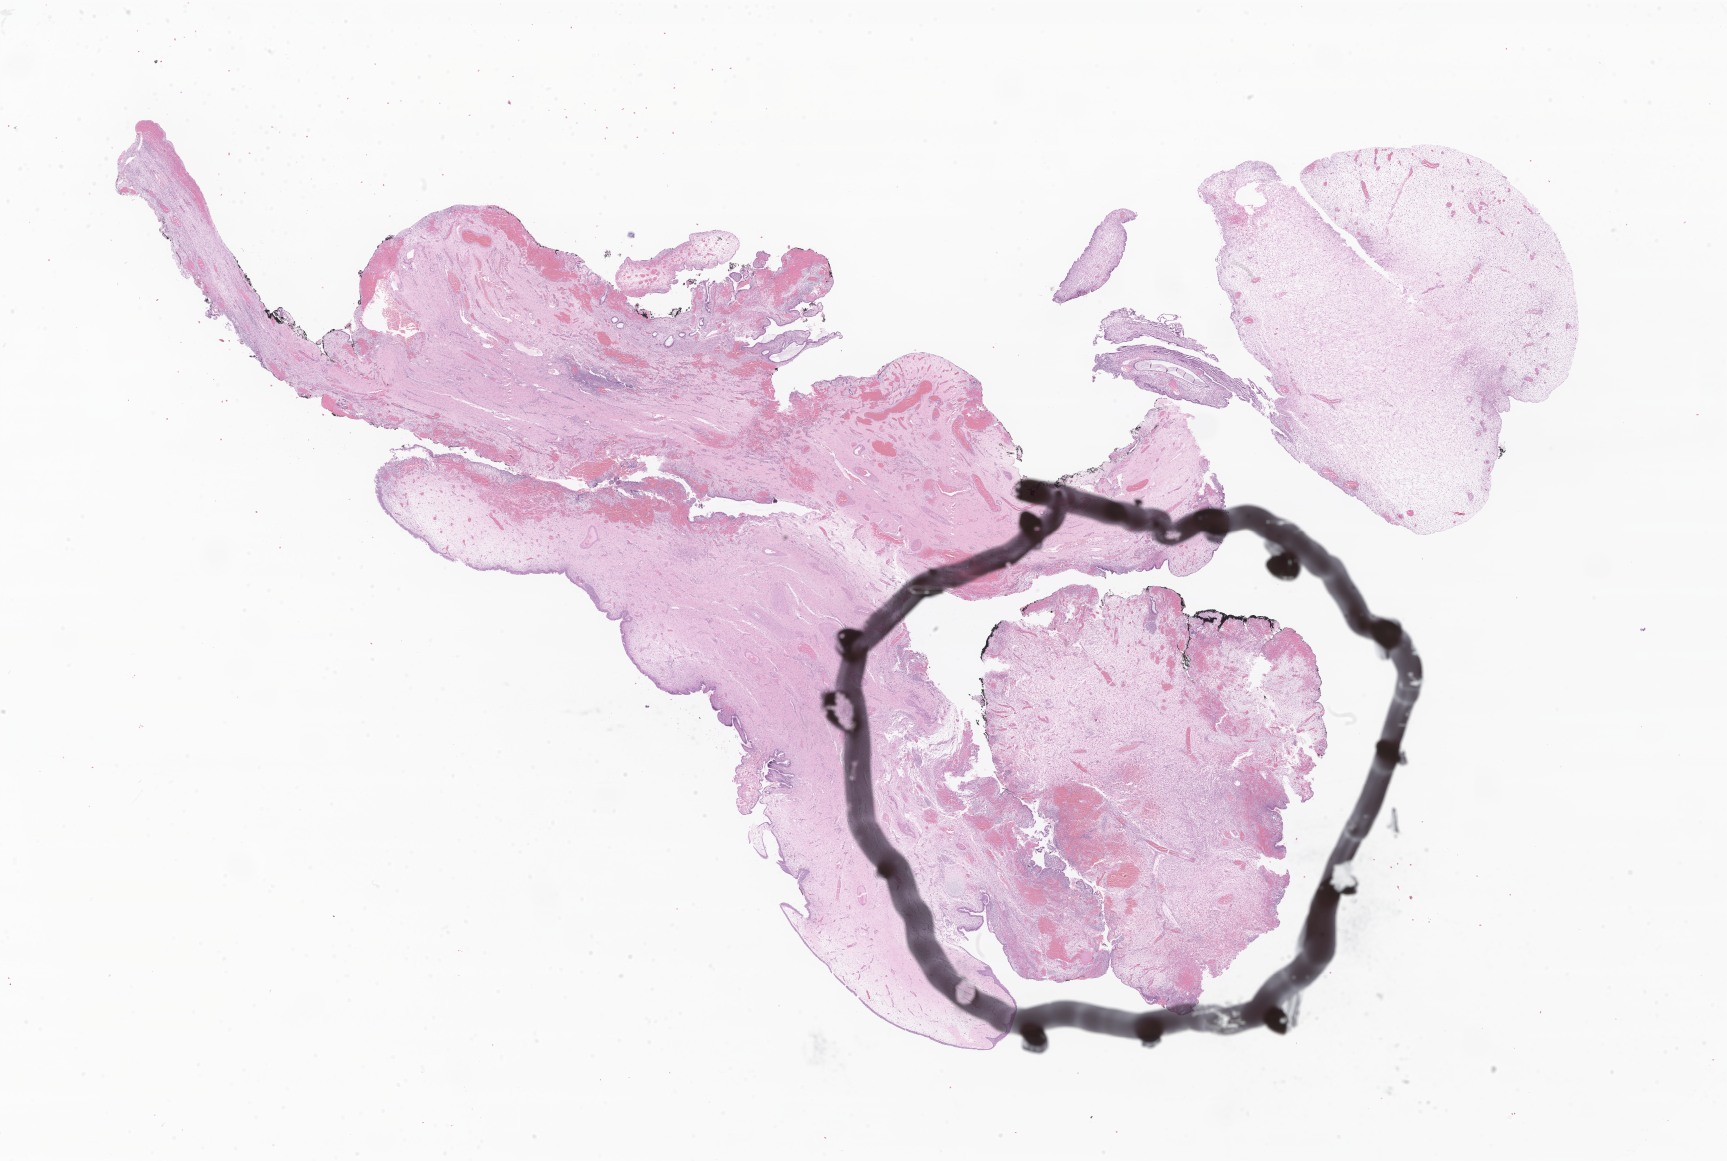
Digitized haematoxylin and eosin-stained section of tumor tissue from the vagina — a low-resolution overview of the entire scanned area, about 29.1 x 19.6 mm; FFPE section. Female patient, age 129 months (10 years 9 months).
Diagnosis (ICD-O-3 morphology term): Embryonal rhabdomyosarcoma, NOS.